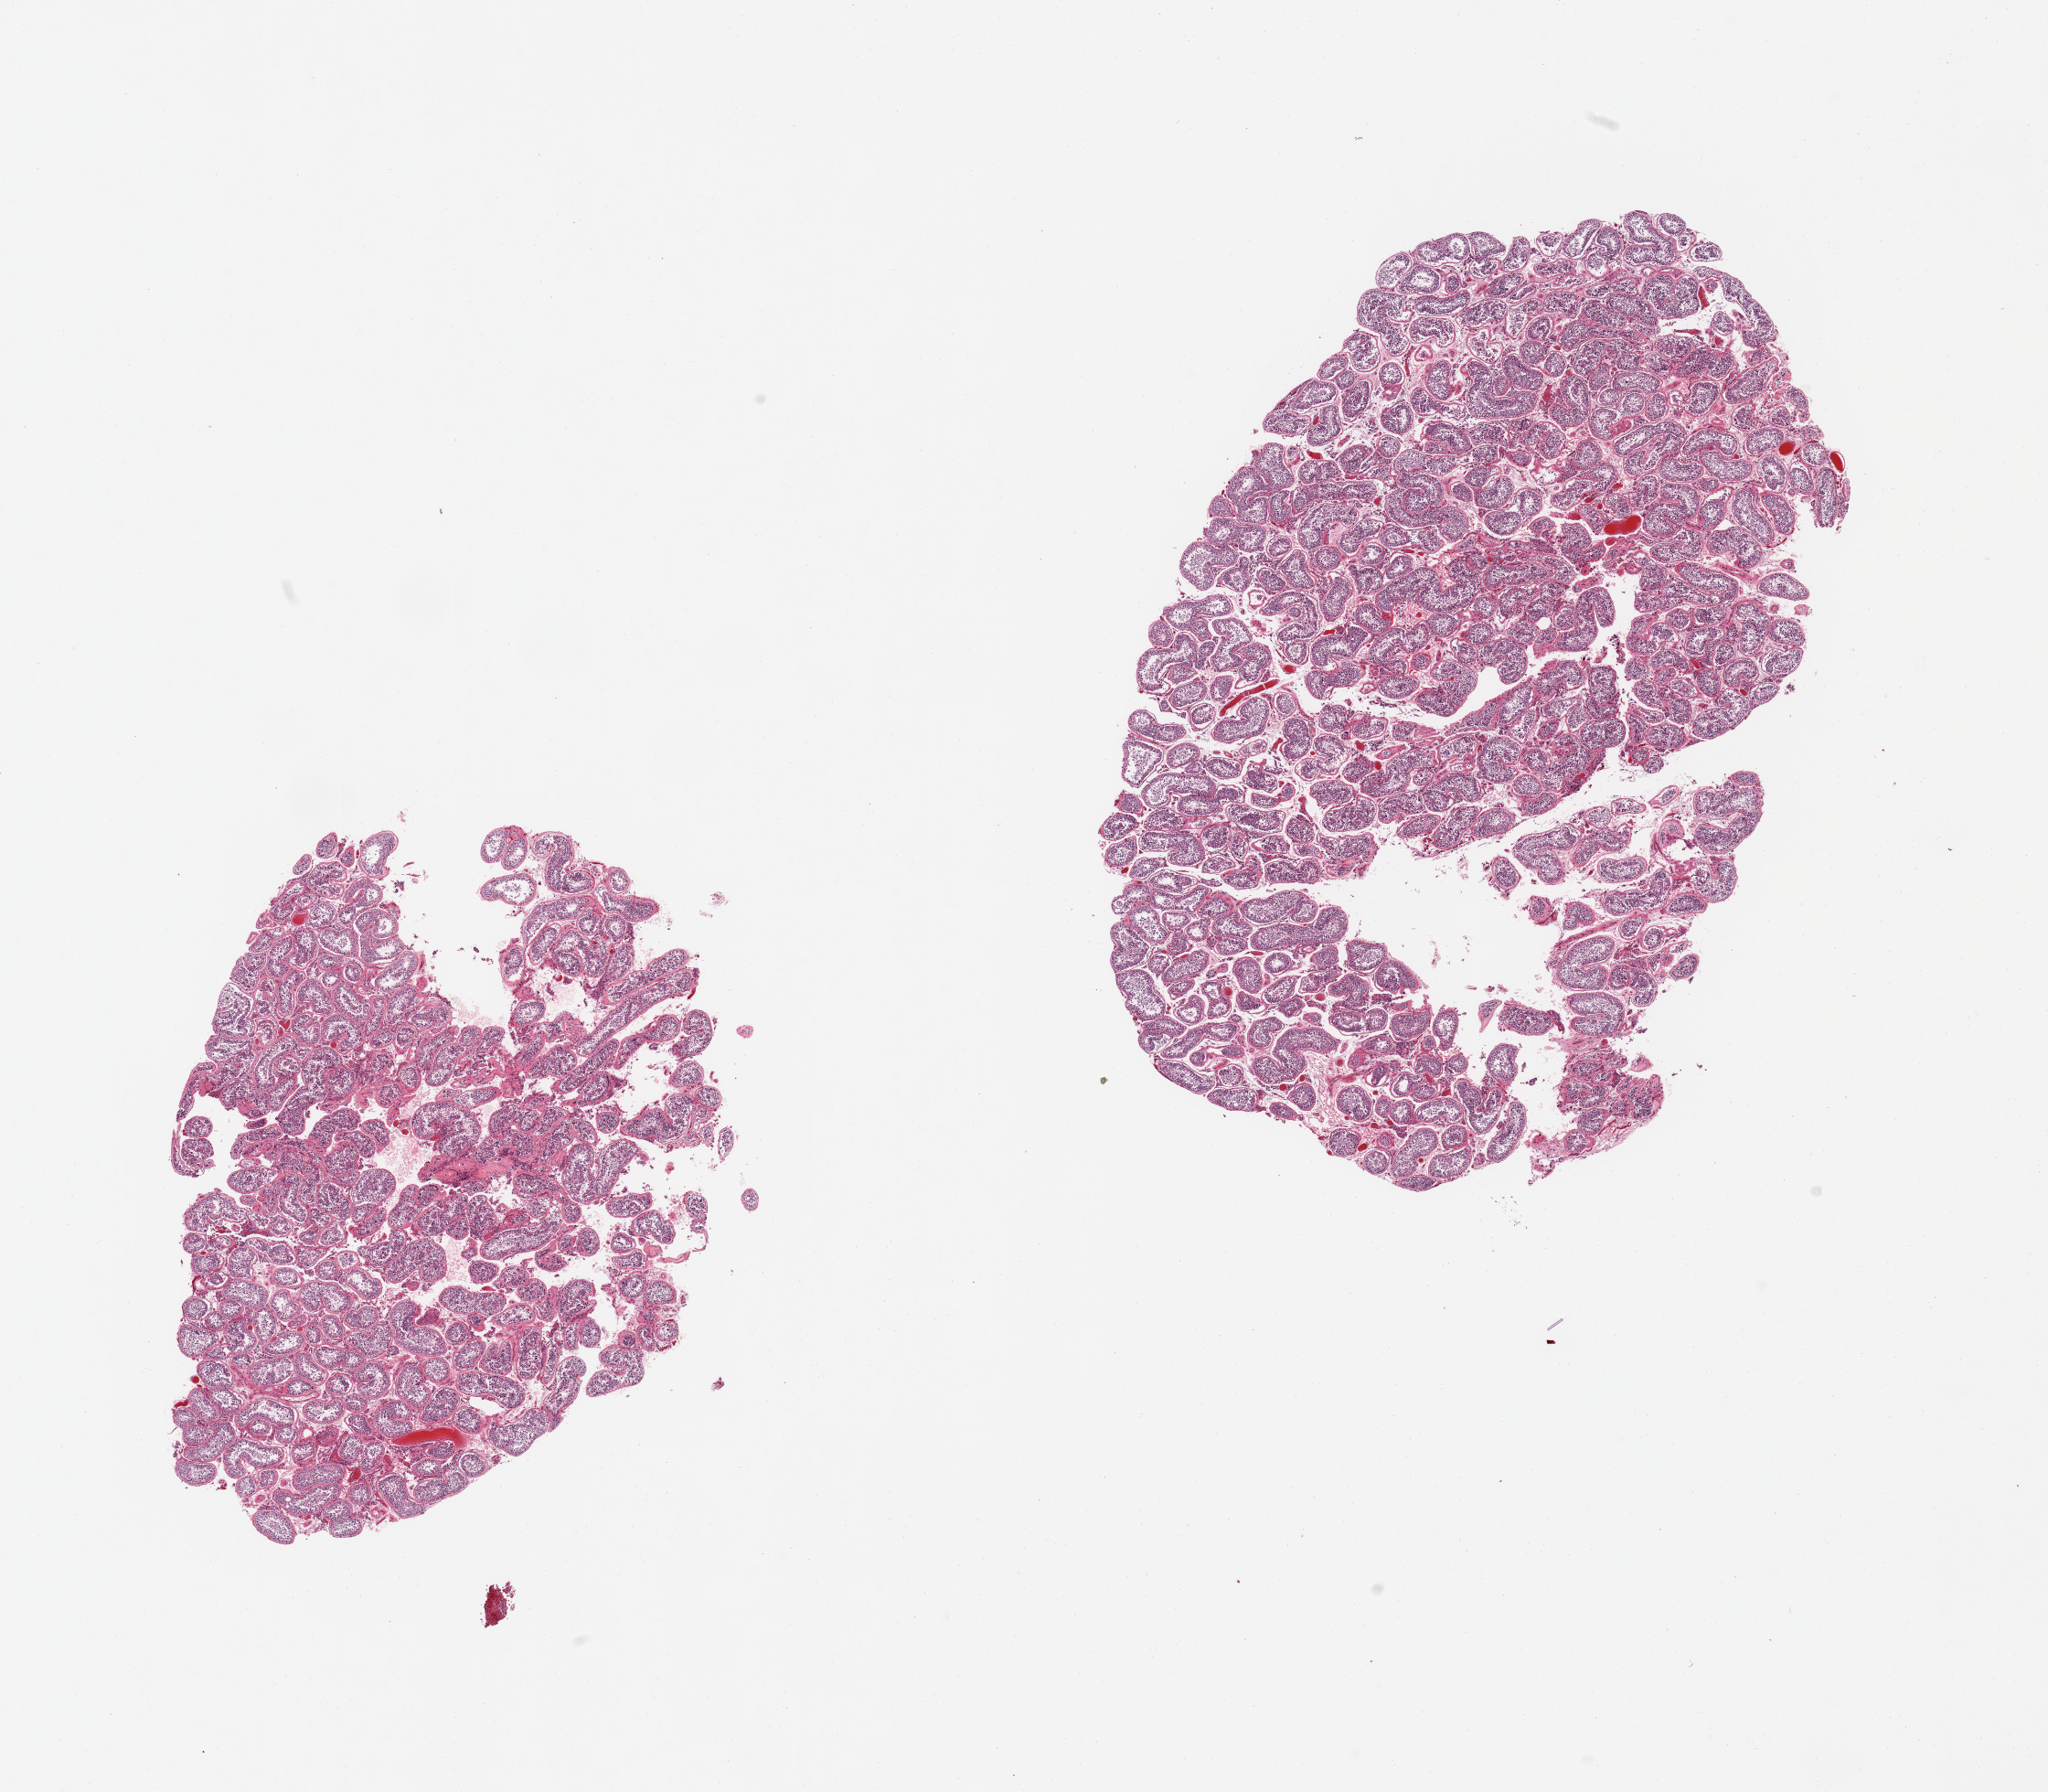
Hematoxylin and eosin (H&E) whole-slide image, shown as a low-resolution overview of the whole scanned area (about 17.7 x 15.5 mm). PAXgene-fixed paraffin-embedded (PFPE) section. Sampled site (target tissue): testis. Donor tissue sample.
Pathologist's review note for this sample: 2 pieces, spermatogenesis present, moderately advanced autolysis.